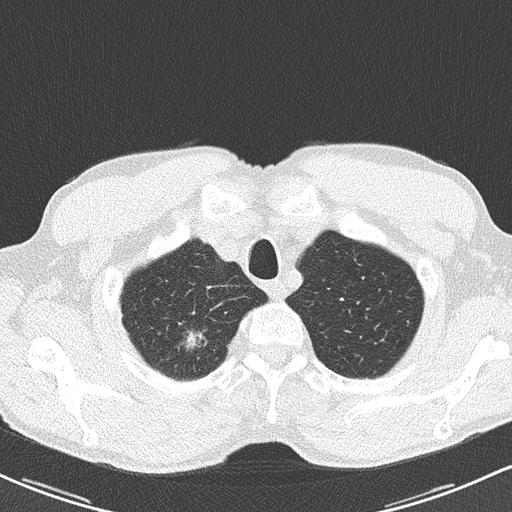
Chest CT (low-dose screening protocol), one axial image. Baseline annual screen. Lung window (W 1500 / L -600 HU). 2 mm slice thickness. 512 × 512 image matrix. Male participant, aged 62 years at enrolment. Former smoker at enrolment.
Expert reader's lesion annotation, bounding box <167,325,215,370> (left, top, right, bottom; pixels). Reader record for this screening exam (exam-level; its link to the box is not recorded): non-calcified nodule or mass ≥4 mm, right upper lobe, 12 × 9 mm, spiculated (stellate) margins, soft tissue attenuation. Official screen result: positive, change unspecified: nodule(s) >= 4 mm or enlarging nodule(s), mass(es), or other non-specific abnormalities suspicious for lung cancer. Later outcome: lung cancer diagnosed 398 days after this screen — bronchiolo-alveolar adenocarcinoma, NOS, right upper lobe, well differentiated (G1), stage IA (AJCC 6th edition), 15 mm at pathology.